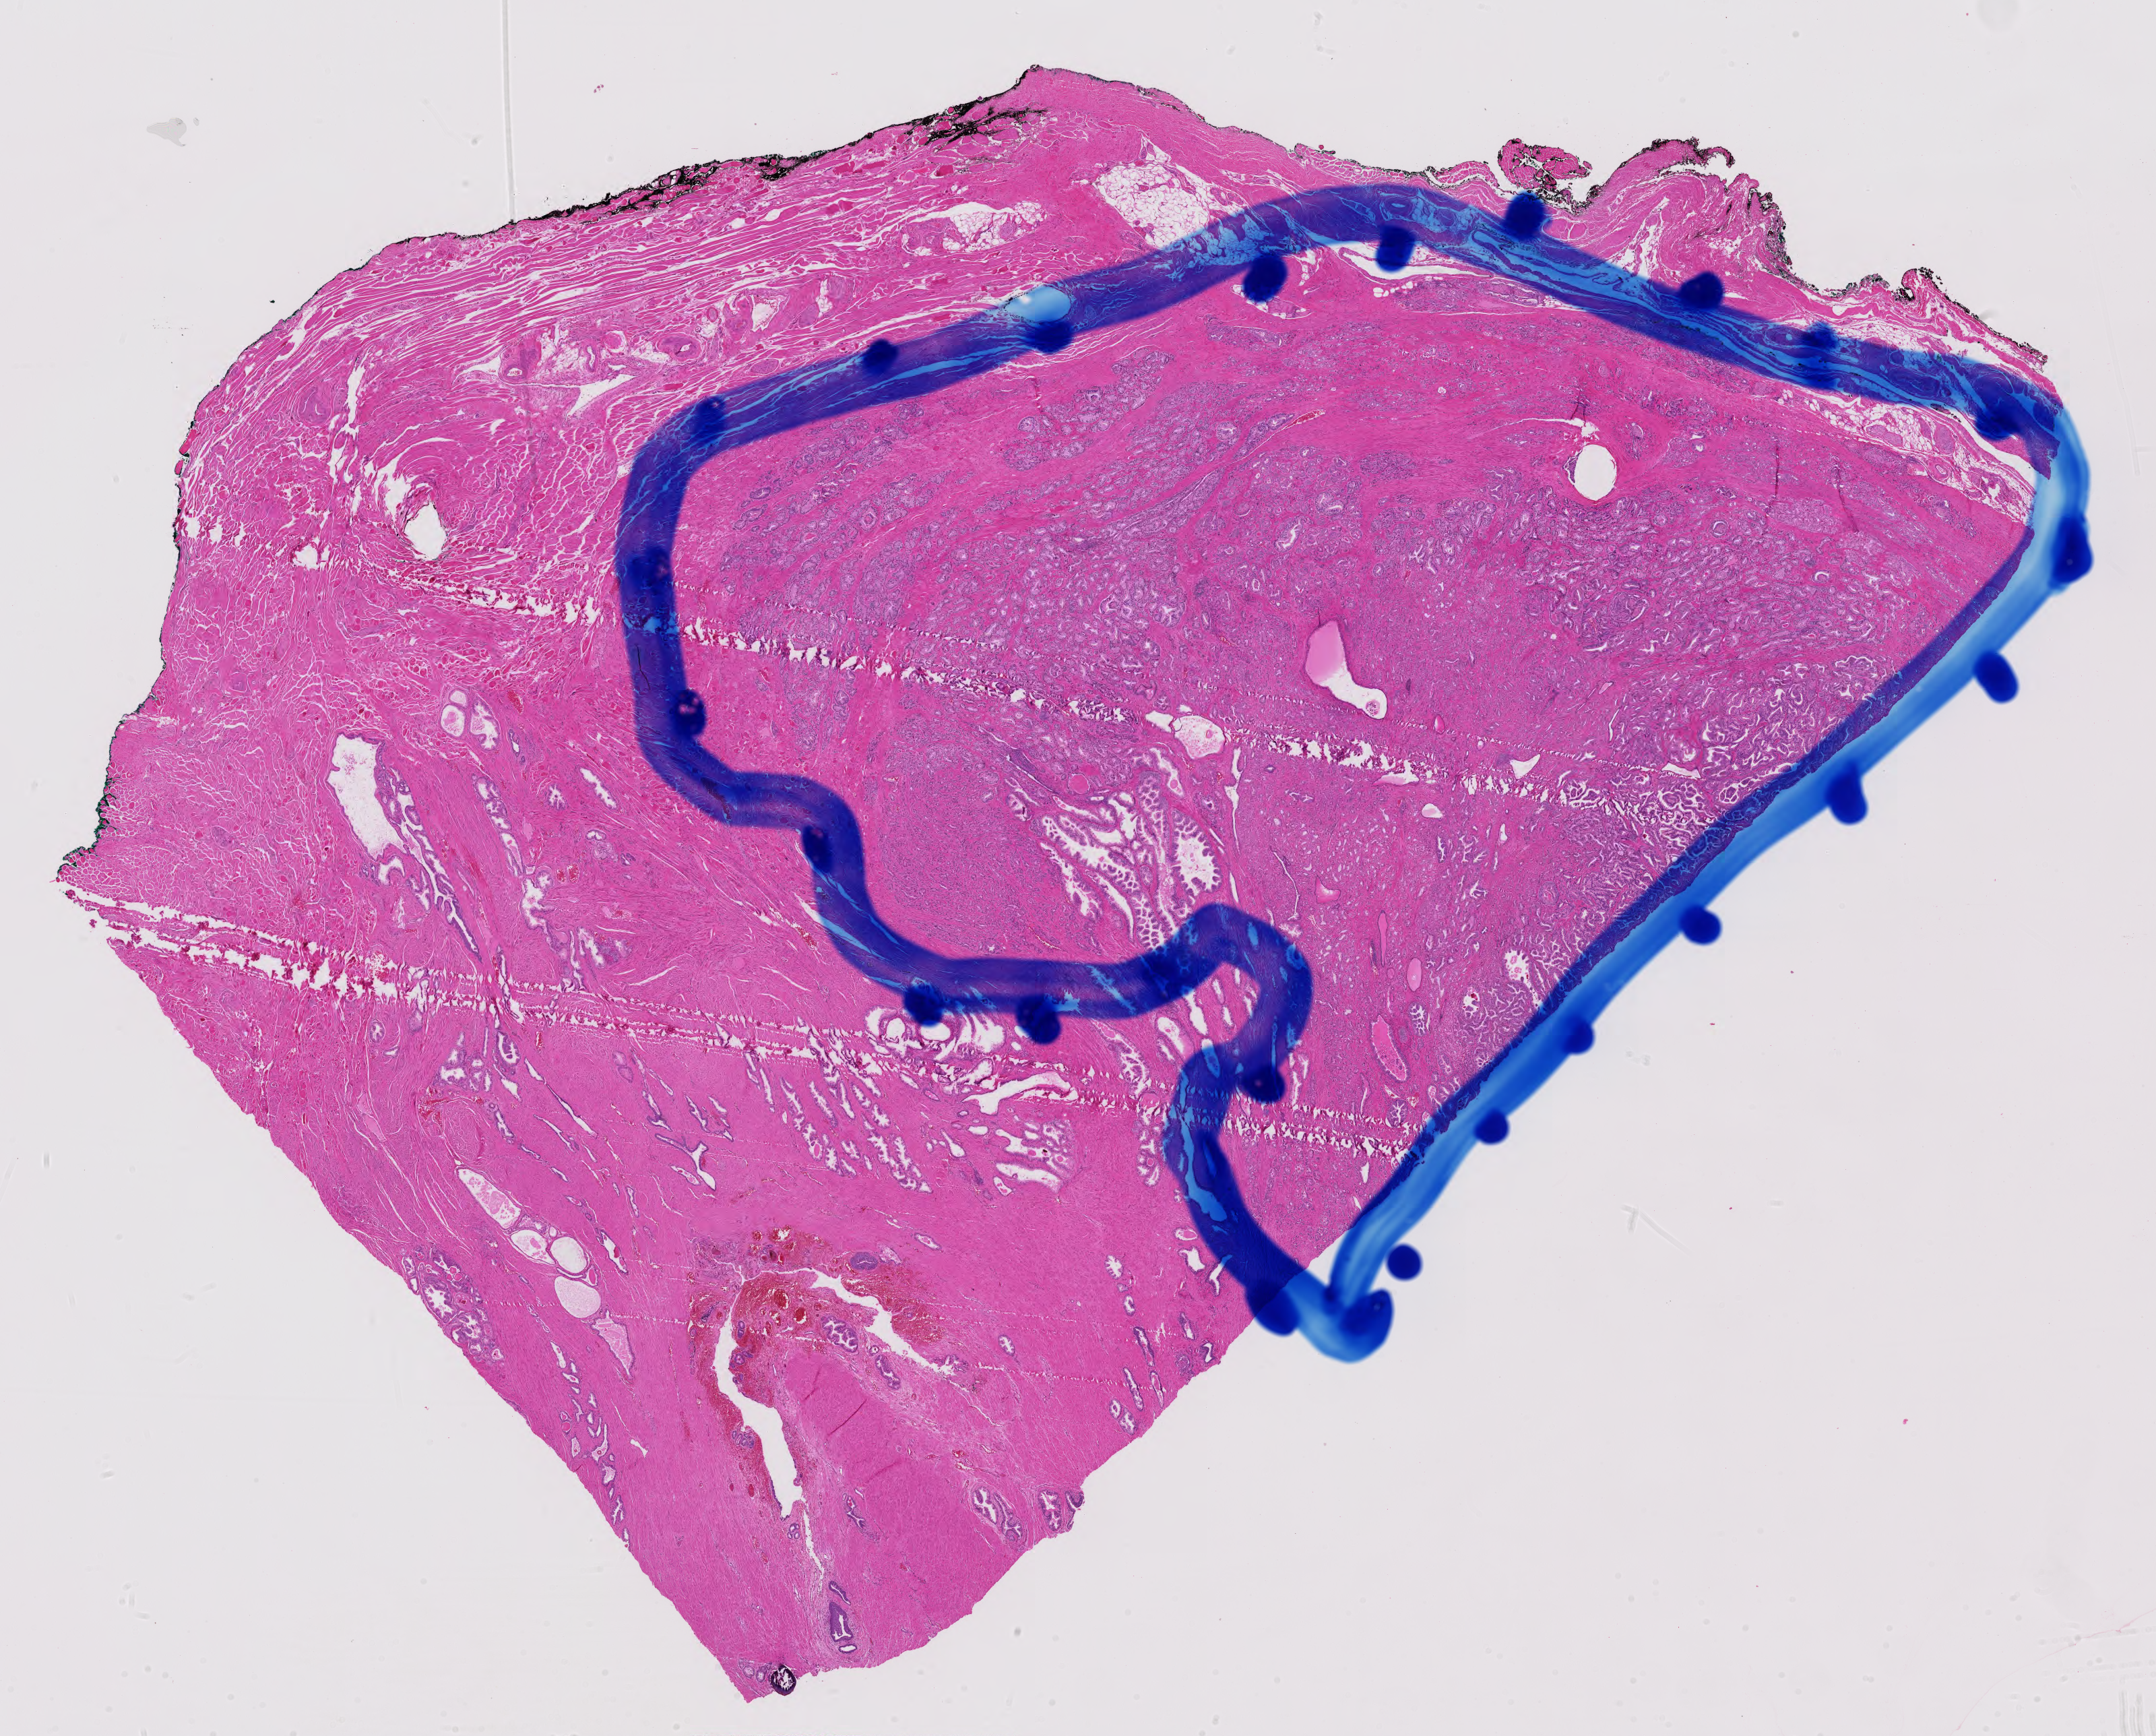
Digitized Hematoxylin and eosin (H&E) stained tissue section (whole slide) — low-resolution overview of the scanned area, about 23.2 x 18.7 mm (acquisition: 40x scan); formalin-fixed paraffin-embedded (FFPE) diagnostic section; sample: primary tumour, prostate. Male patient; age at initial diagnosis 69 years. Gleason score: 7 (4+3).
- laterality: bilateral
- pathologic diagnosis: Adenocarcinoma, NOS (prostate gland)